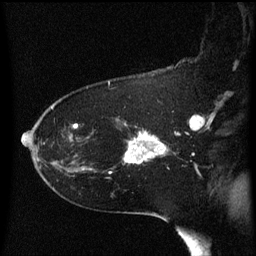
Breast MRI (dynamic contrast-enhanced), one sagittal slice; position 41 of 60 along the scan axis; dynamic contrast-enhanced series, image 2 of 3 at this slice position (ordered by acquisition); 1.5 T; TE 4.2 ms, TR 8.4 ms; 2 mm slice thickness; 256 × 256 image matrix, field of view 200 × 200 mm. Female patient, age 54 years. Case-level facts recorded for this patient, not image findings: setting: breast cancer imaged before/during neoadjuvant chemotherapy; receptor status: HR-positive, HER2-negative.
Structures marked on this image (semi-automatically segmented with operator editing):
- analysis volume of interest (the breast-tissue region the enhancement analysis was run in; not a lesion): bounding box [x1, y1, x2, y2] px = [125, 132, 172, 165]
- tumour enhancement mask (voxels above the 70 % enhancement threshold inside the analysis volume of interest): [125, 132, 167, 165]